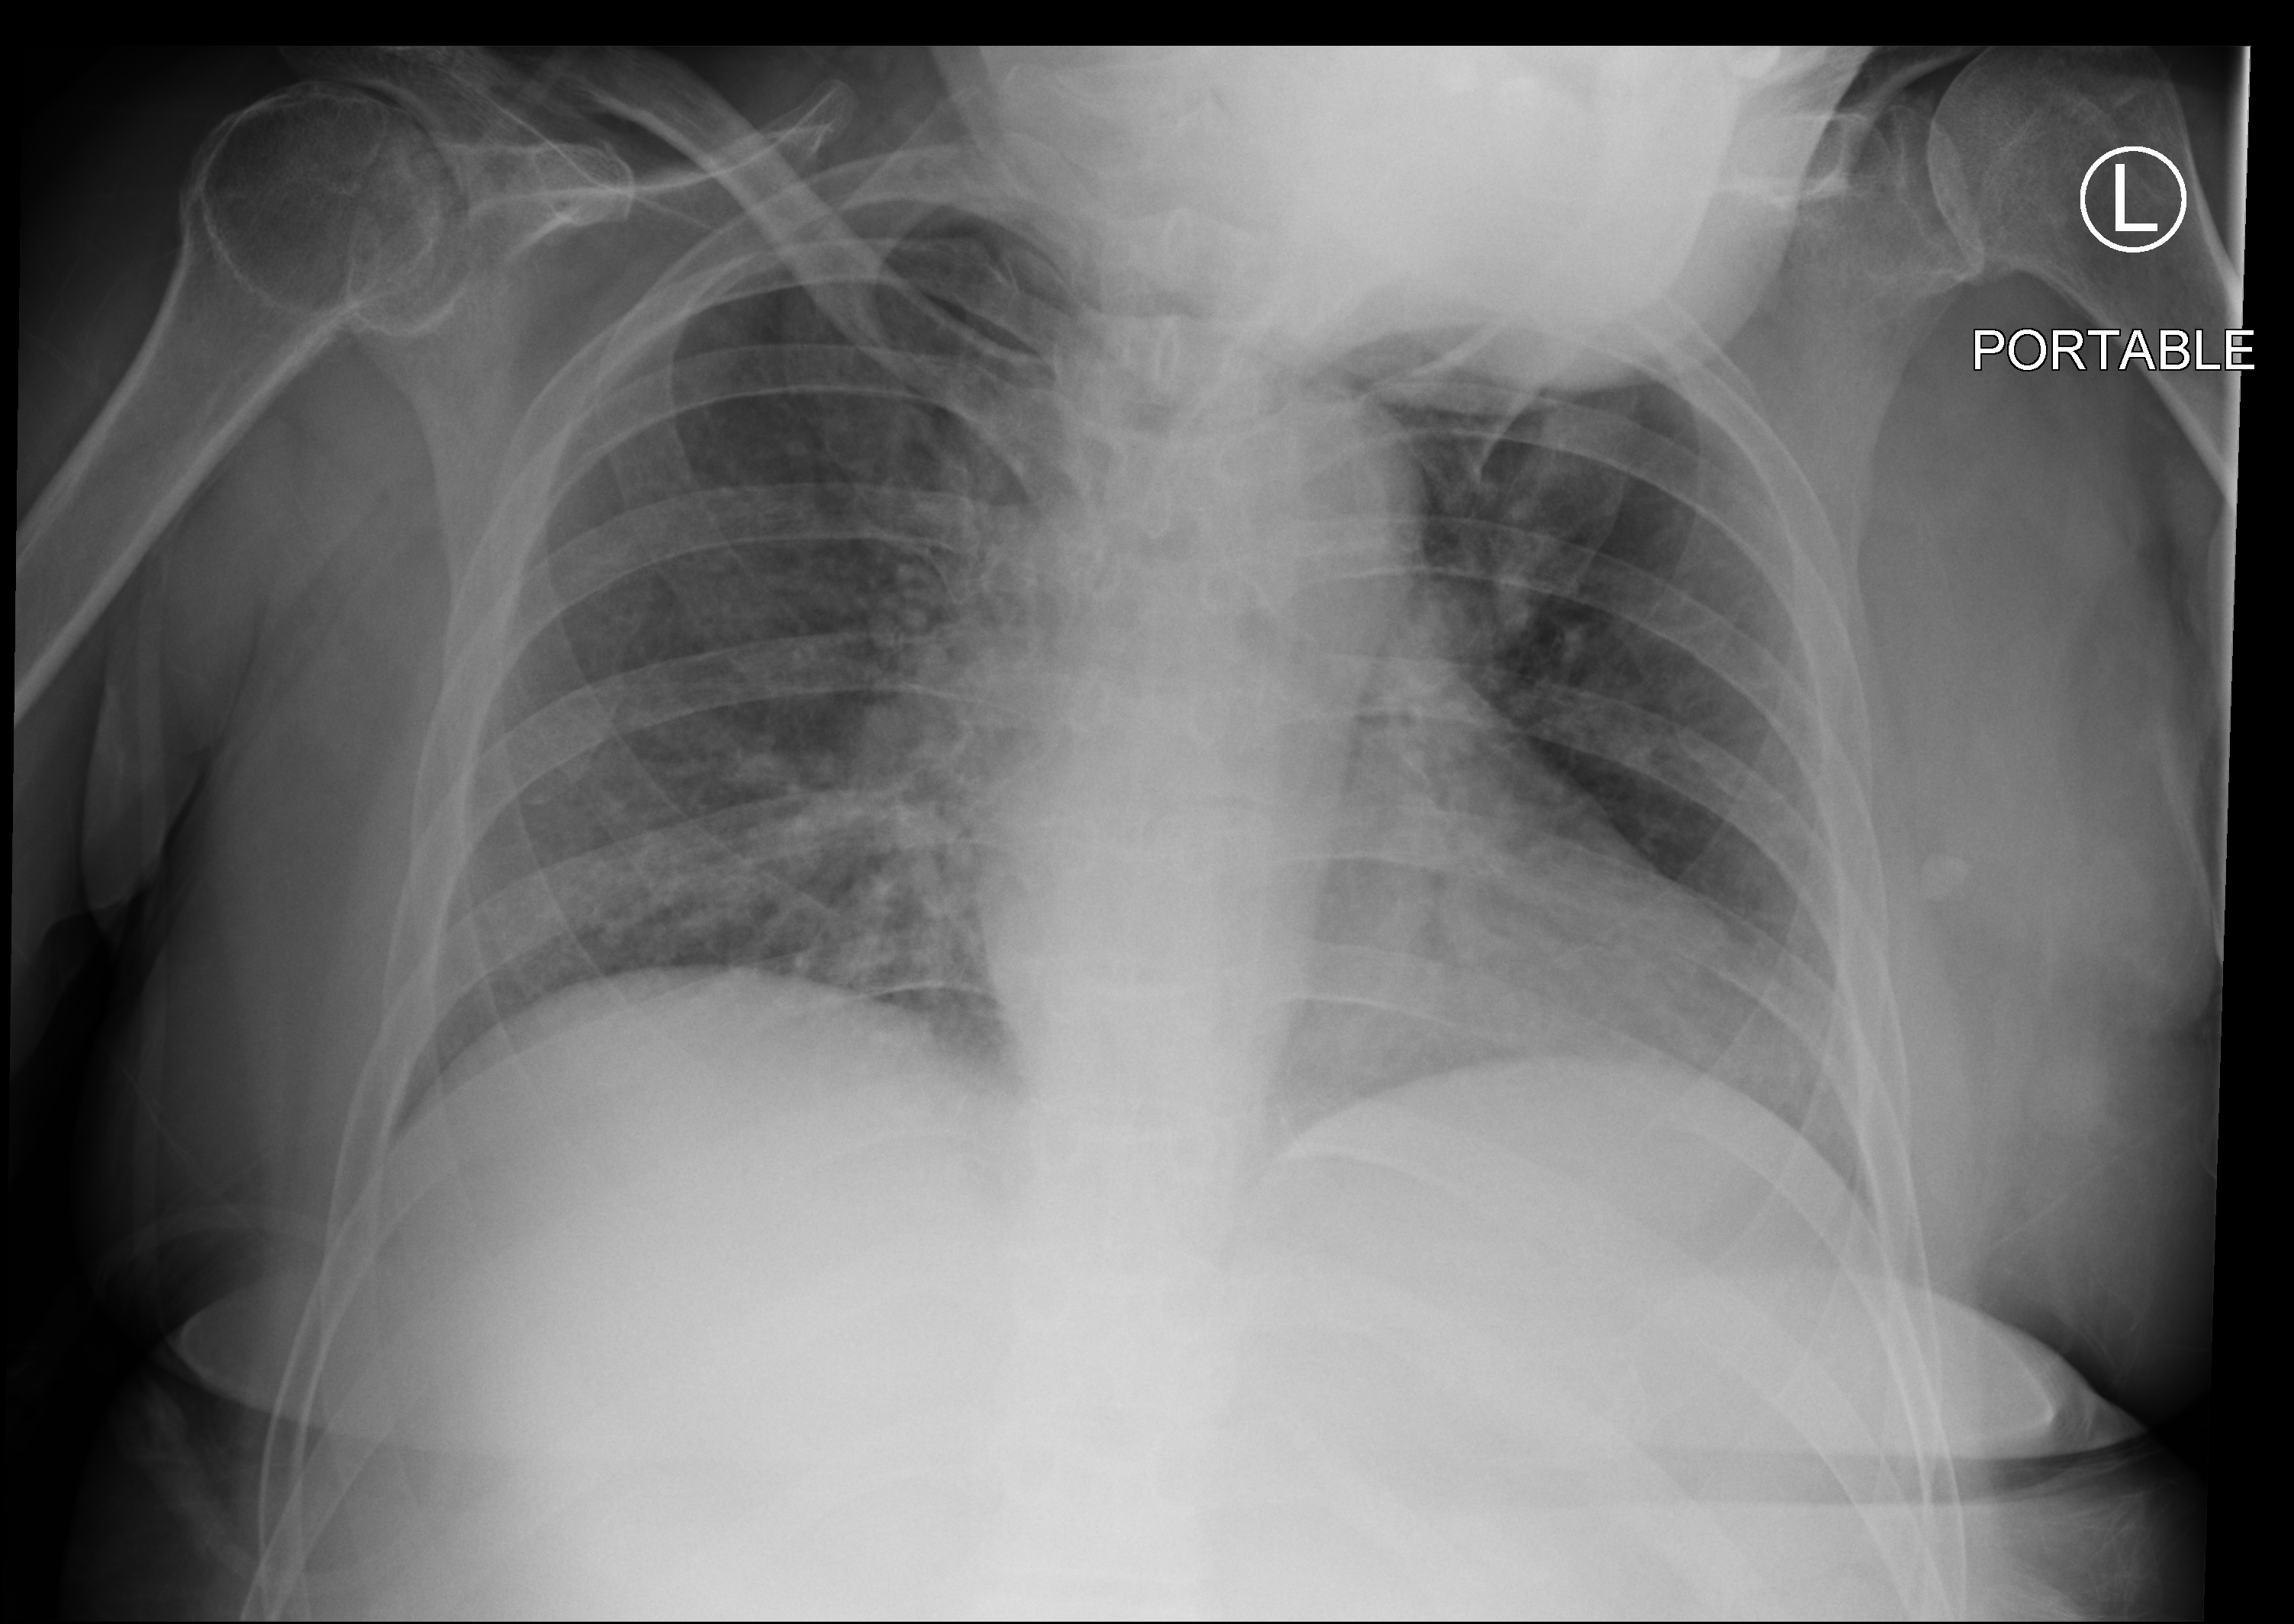
Portable chest radiograph, anteroposterior (AP) projection. Female patient hospitalised with COVID-19, age 60–74 years.
From the hospital-stay record, not from the radiograph (when in the stay this image was taken is not recorded):
- mechanically ventilated during this hospital stay: no
- admitted to intensive care during this hospital stay: no